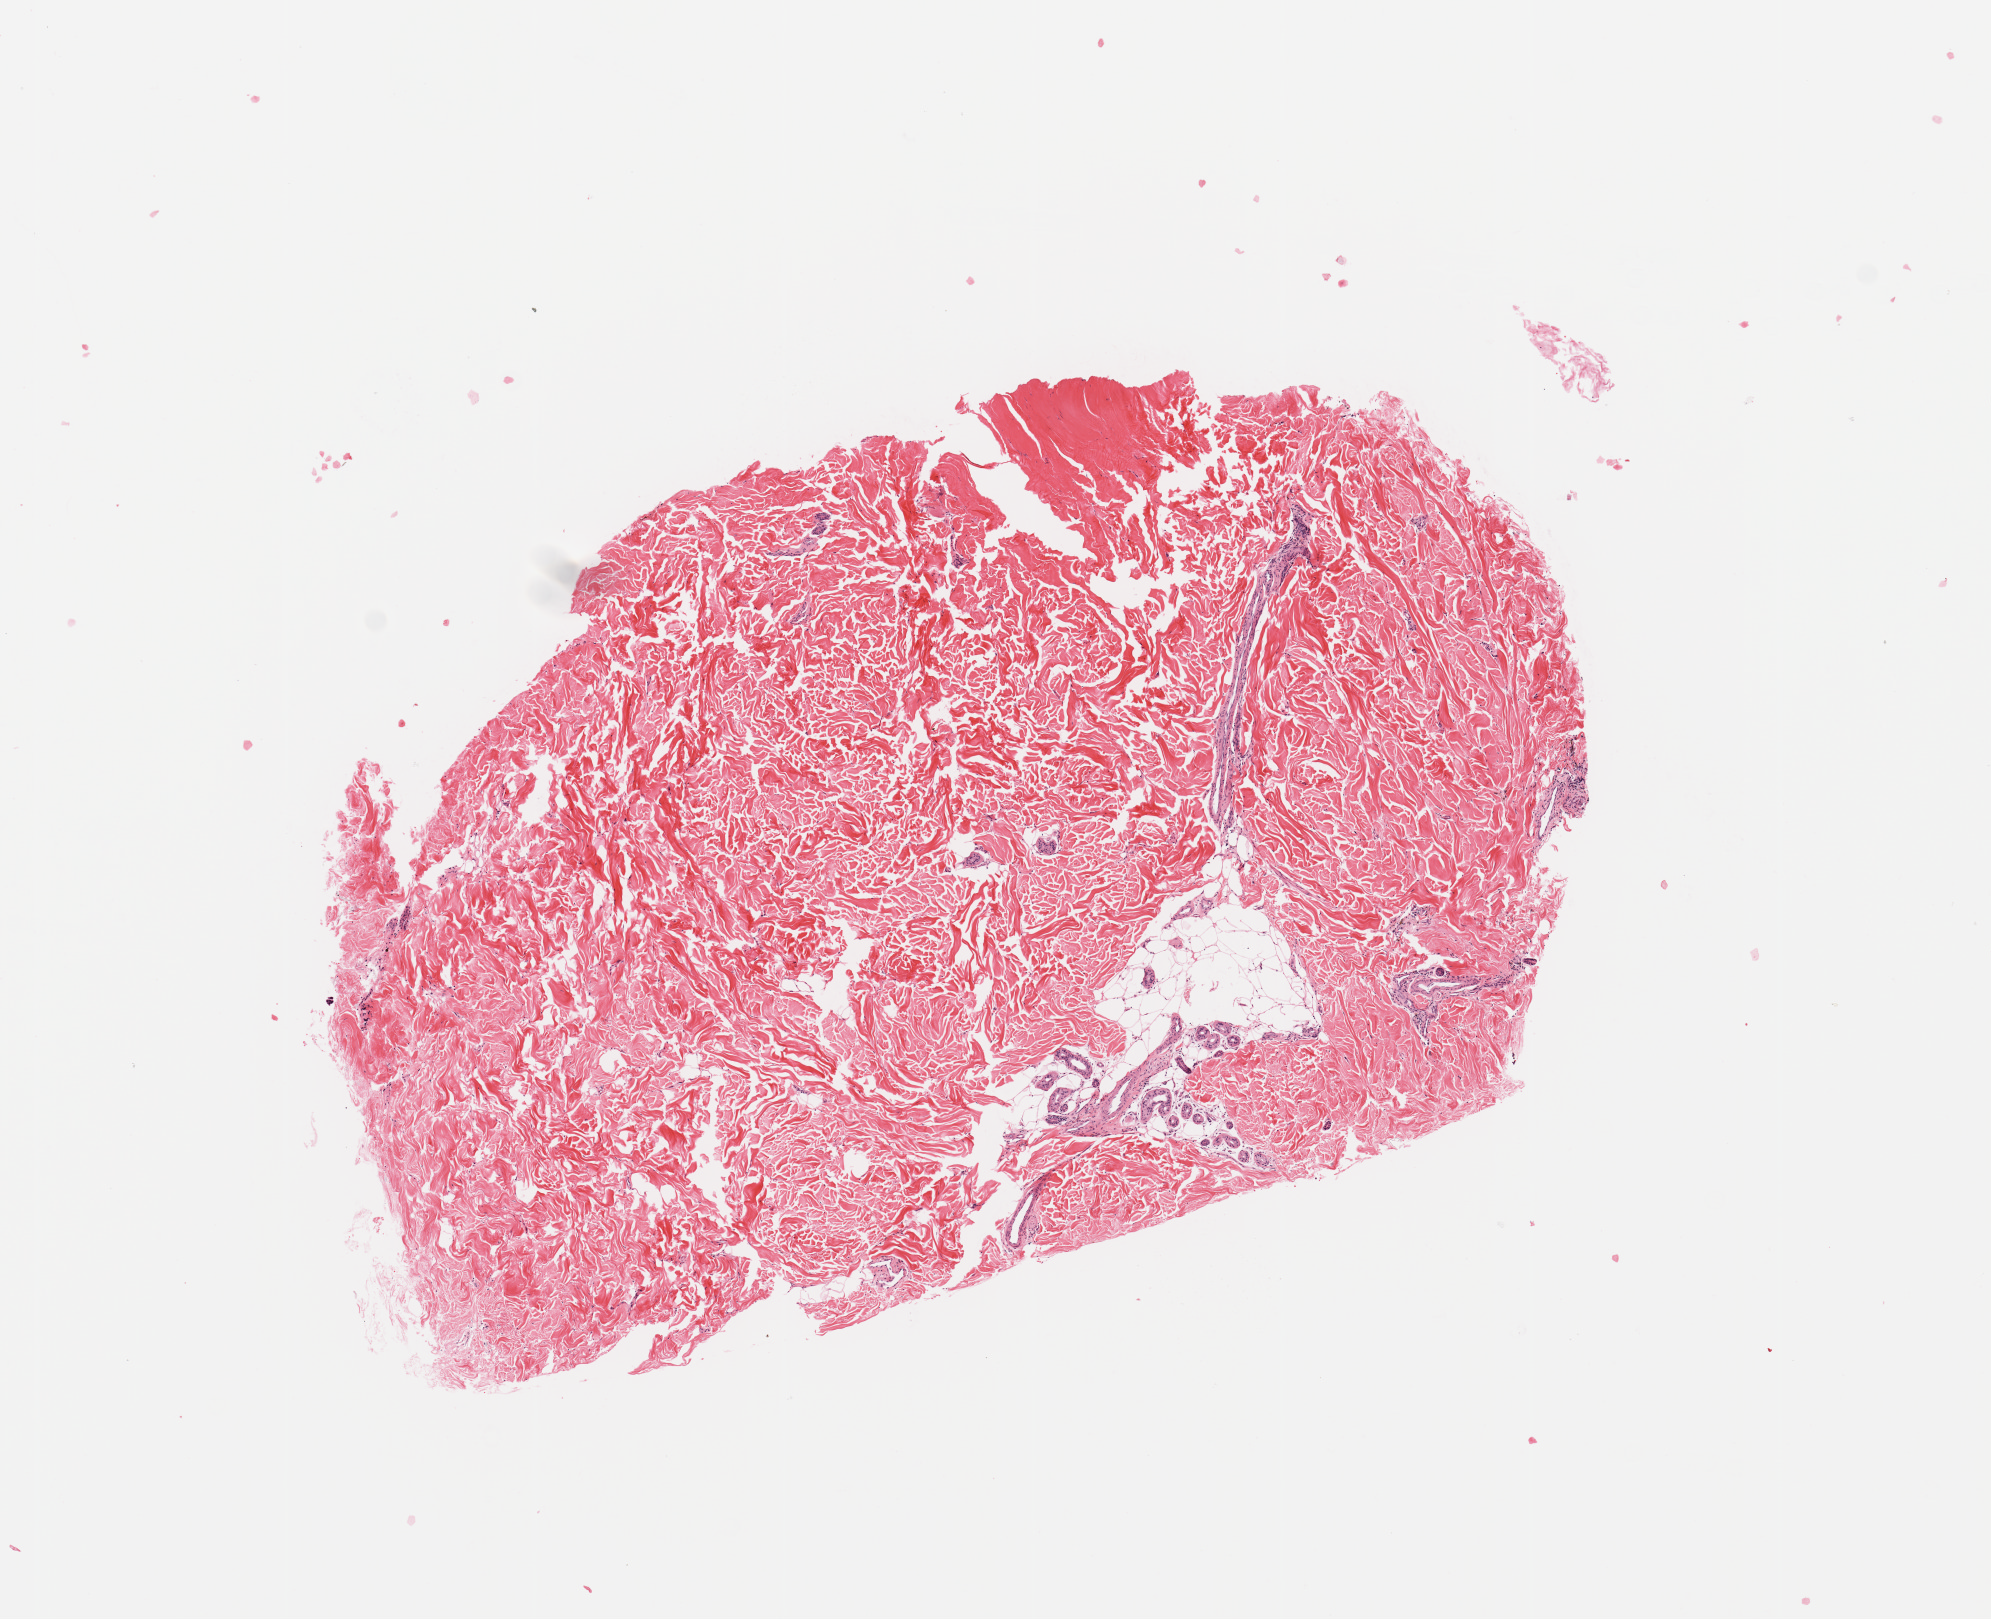
Digitized H&E tissue section (whole slide) — a low-resolution overview of the entire scanned area, about 7.9 x 6.4 mm; melanoma tumour tissue; sampled site not recorded. 66-year-old female patient.
Patient diagnosis (cohort enrolment): cutaneous melanoma (skin). Primary tumour site (as recorded): head & neck.